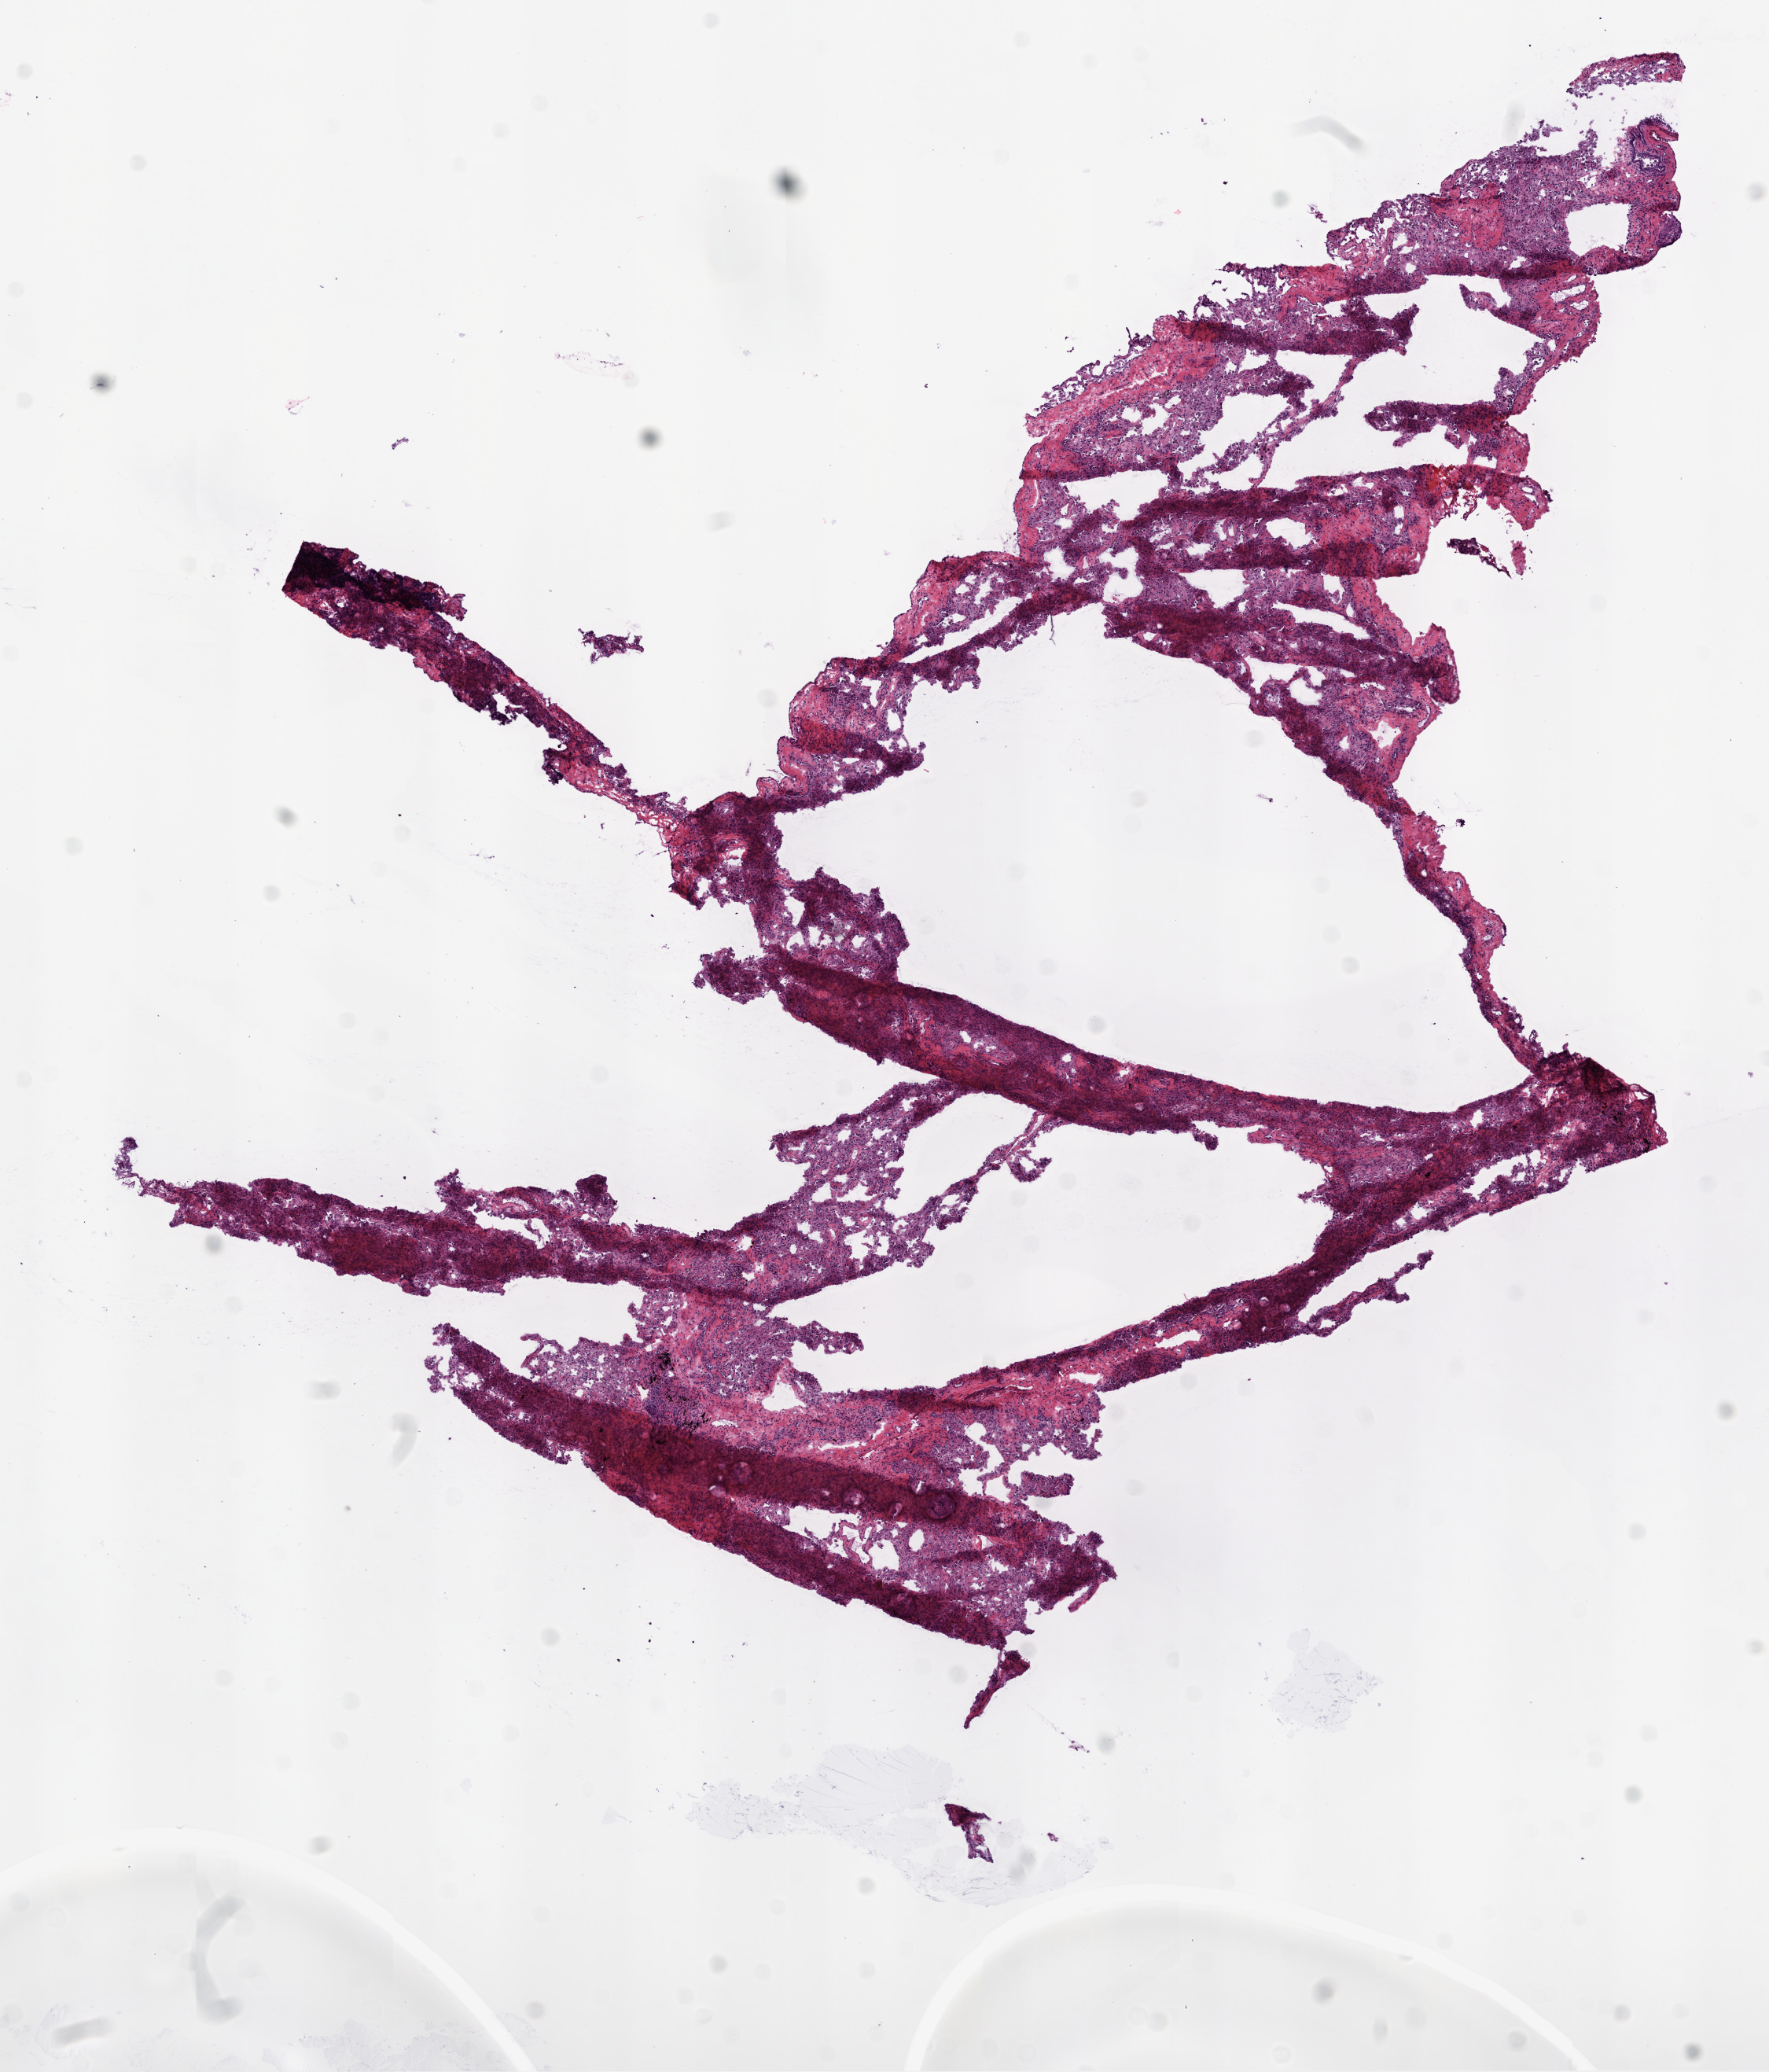
Digitized Hematoxylin and eosin (H&E) stained tissue section (whole slide) — whole scanned area (about 9.0 x 10.6 mm, acquisition: 20x scan) shown as a low-resolution overview, frozen section from the bottom of the tissue portion, lung, solid tissue normal (non-tumour tissue) sample. Male, age 71 years at initial diagnosis.
* this section: solid tissue normal sample (biorepository sample class)
* patient diagnosis: Squamous cell carcinoma, NOS (middle lobe, lung)